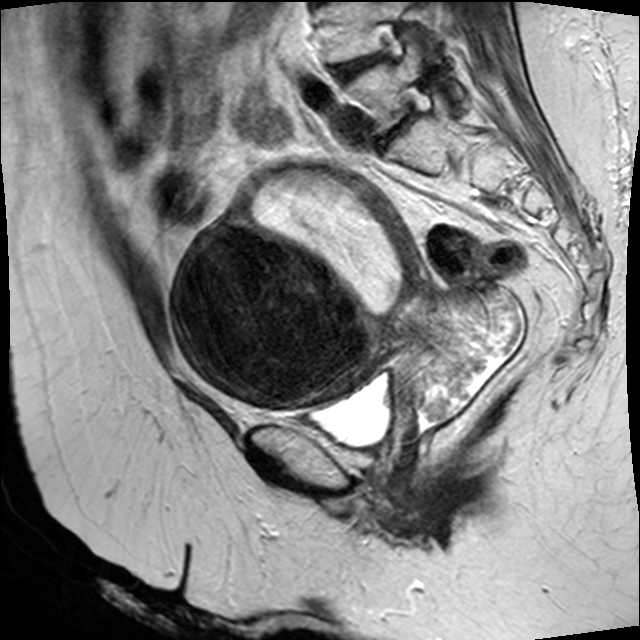
Pelvic MRI for cervical cancer, one sagittal slice. Position 20 of 45 along the scan axis. T2-weighted. 1.5 T. TE 89 ms, TR 4610 ms. 4 mm slice thickness. 640 × 640 image matrix. Female patient, age 50 years.
Structures marked on this image (manually delineated by an expert):
- uterus and cervix: box from (x=173, y=162) to (x=522, y=438) px